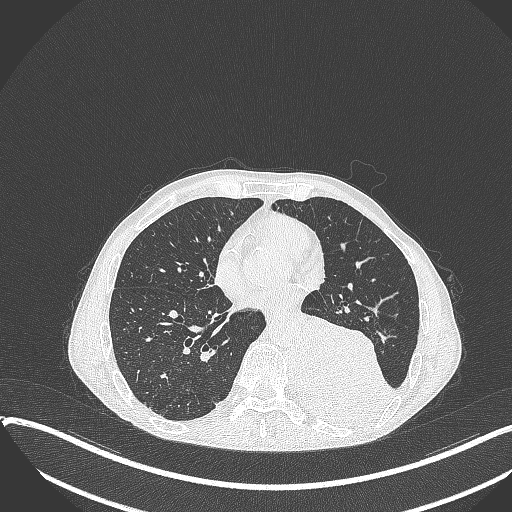
Chest CT, one axial slice. Slice 151 of 401 in the series (ordered by position). Lung window (W 1500 / L -600 HU). 512 × 512 image matrix, field of view 400 × 400 mm. Male patient, age 57 years. From the clinical record (not read from this slice): clinical TNM (as recorded): T4 N0 M0.
Outlined on this slice (bounding box drawn by a radiologist):
- lung tumour (recorded histology: squamous cell carcinoma): box from (x=294, y=308) to (x=393, y=428) px